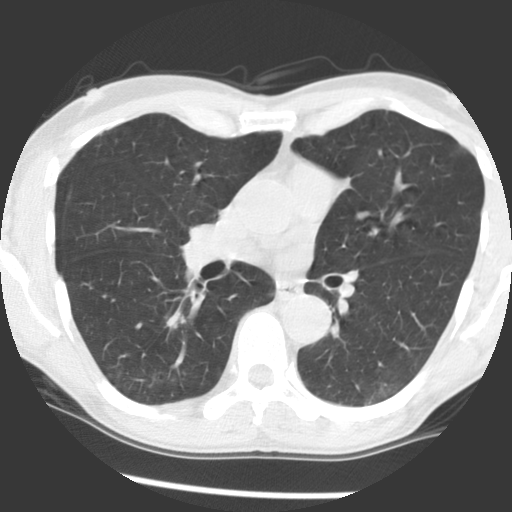
Low-dose screening chest CT, axial slice; baseline annual screen; lung window (W 1500 / L -600 HU); slice 94 of 165 in the series. Male participant, aged 65 years at enrolment.
Expert-annotated lung lesion, box from (x=153, y=302) to (x=206, y=344) px. The screening reader recorded 2 non-calcified nodules or masses ≥4 mm on this exam (right lower lobe, left lower lobe); which of them this box marks is not recorded. Official screen result: positive, change unspecified: nodule(s) >= 4 mm or enlarging nodule(s), mass(es), or other non-specific abnormalities suspicious for lung cancer. Later outcome: lung cancer diagnosed 774 days after this screen — adenocarcinoma, NOS, right lower lobe, poorly differentiated (G3), stage IA (AJCC 6th edition), 18 mm at pathology.